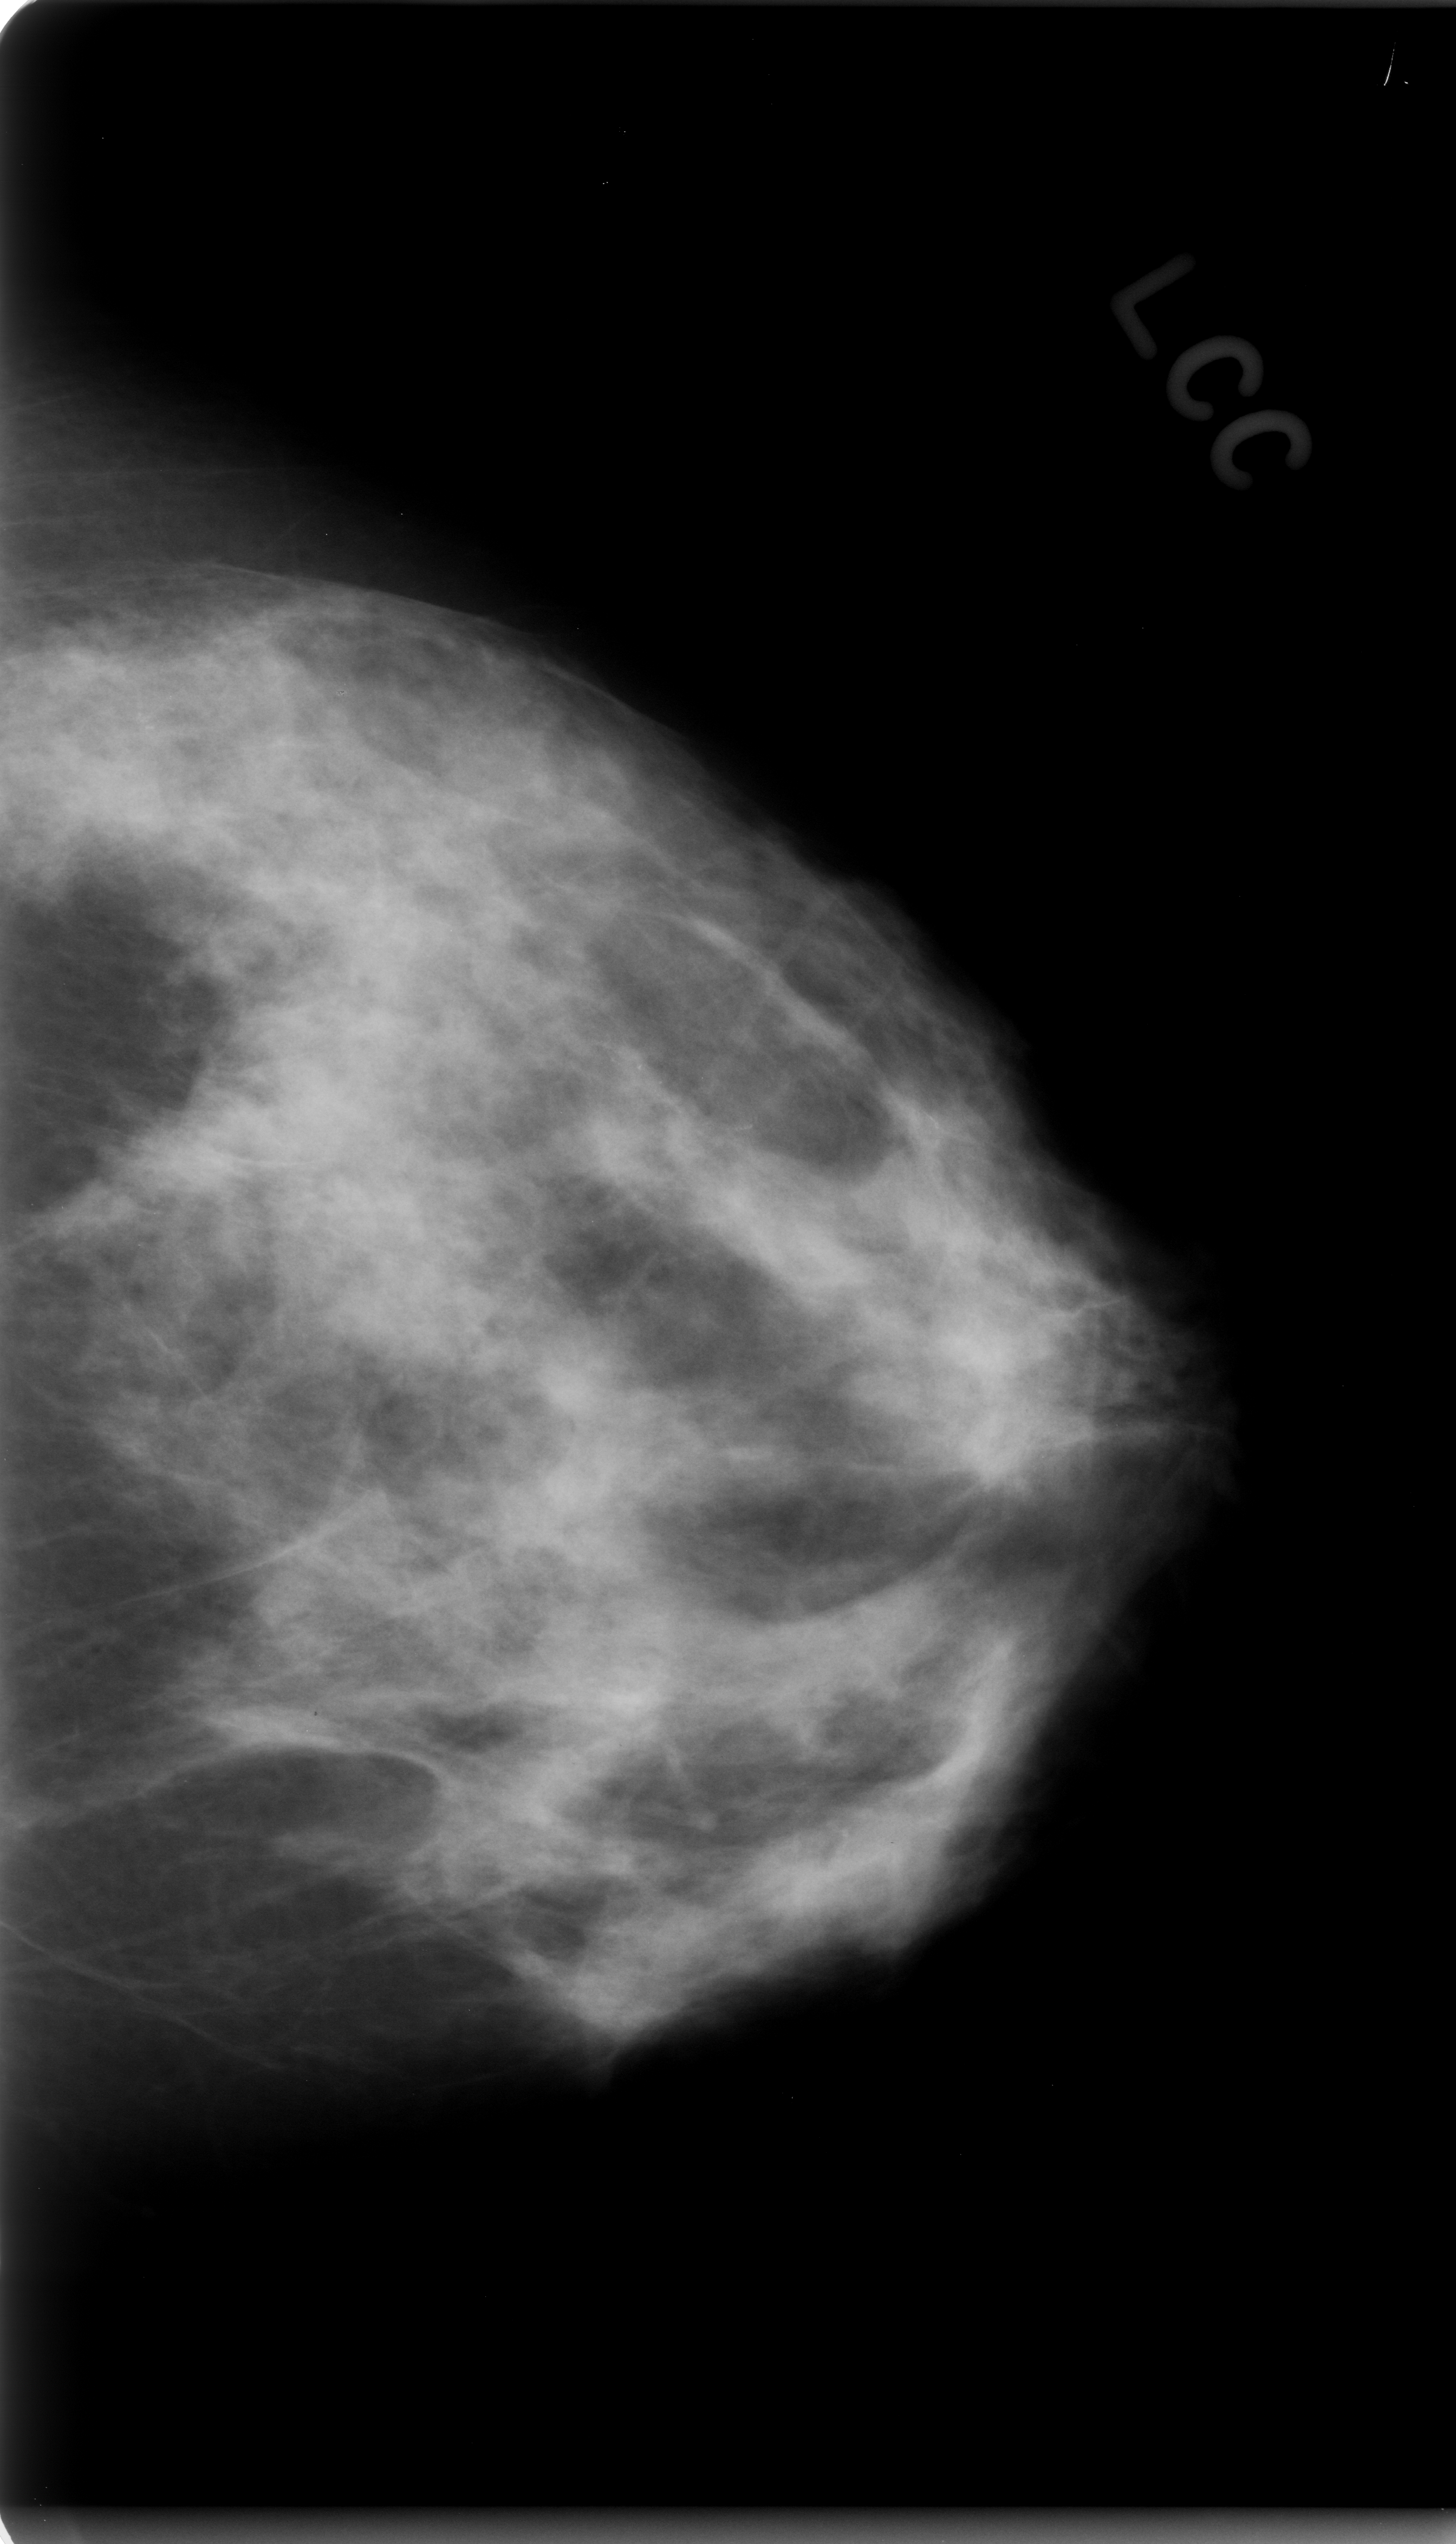
Scanned film-screen mammogram; left breast; CC view; breast composition: heterogeneously dense (BI-RADS density category 3 of 4); 1456 × 2544 image matrix.
Expert-marked regions of interest on this film, with their recorded descriptors:
- Finding 1 of 2: calcifications, morphology amorphous, distribution clustered; BI-RADS assessment category 4; subtlety rating 1 on a 1 (subtle) to 5 (obvious) scale; pathology result (as recorded, not read from the image): benign: bounding box (x1, y1, x2, y2) in pixels: (69, 628, 317, 859)
- Finding 2 of 2: calcifications, morphology amorphous, distribution clustered; BI-RADS assessment category 4; subtlety rating 1 on a 1 (subtle) to 5 (obvious) scale; pathology result (as recorded, not read from the image): malignant: (533, 988, 751, 1249)